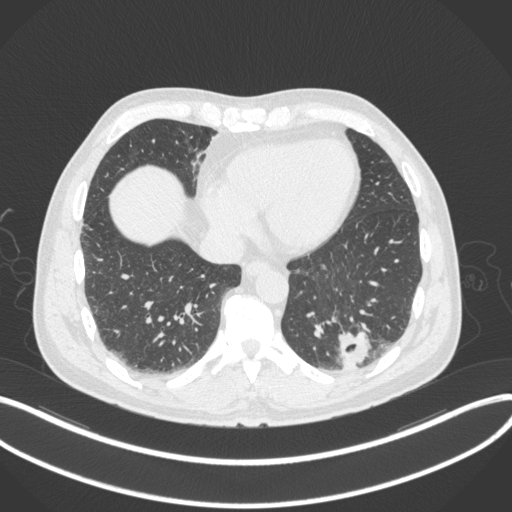
Chest CT, one axial slice. Slice 82 of 313 in the series (ordered by position). Reconstruction kernel B31f. 120 kVp. Lung window (W 1500 / L -600 HU). 1 mm slice thickness. 512 × 512 image matrix, field of view 400 × 400 mm. Patient: male, 54 years. Case-level facts recorded for this patient, not image findings: clinical TNM (as recorded): T1c N0 M1; histopathological grade: G3.
Structures marked on this image (bounding box drawn by a radiologist):
- lung tumour (recorded histology: adenocarcinoma): box from (x=333, y=326) to (x=376, y=370) px